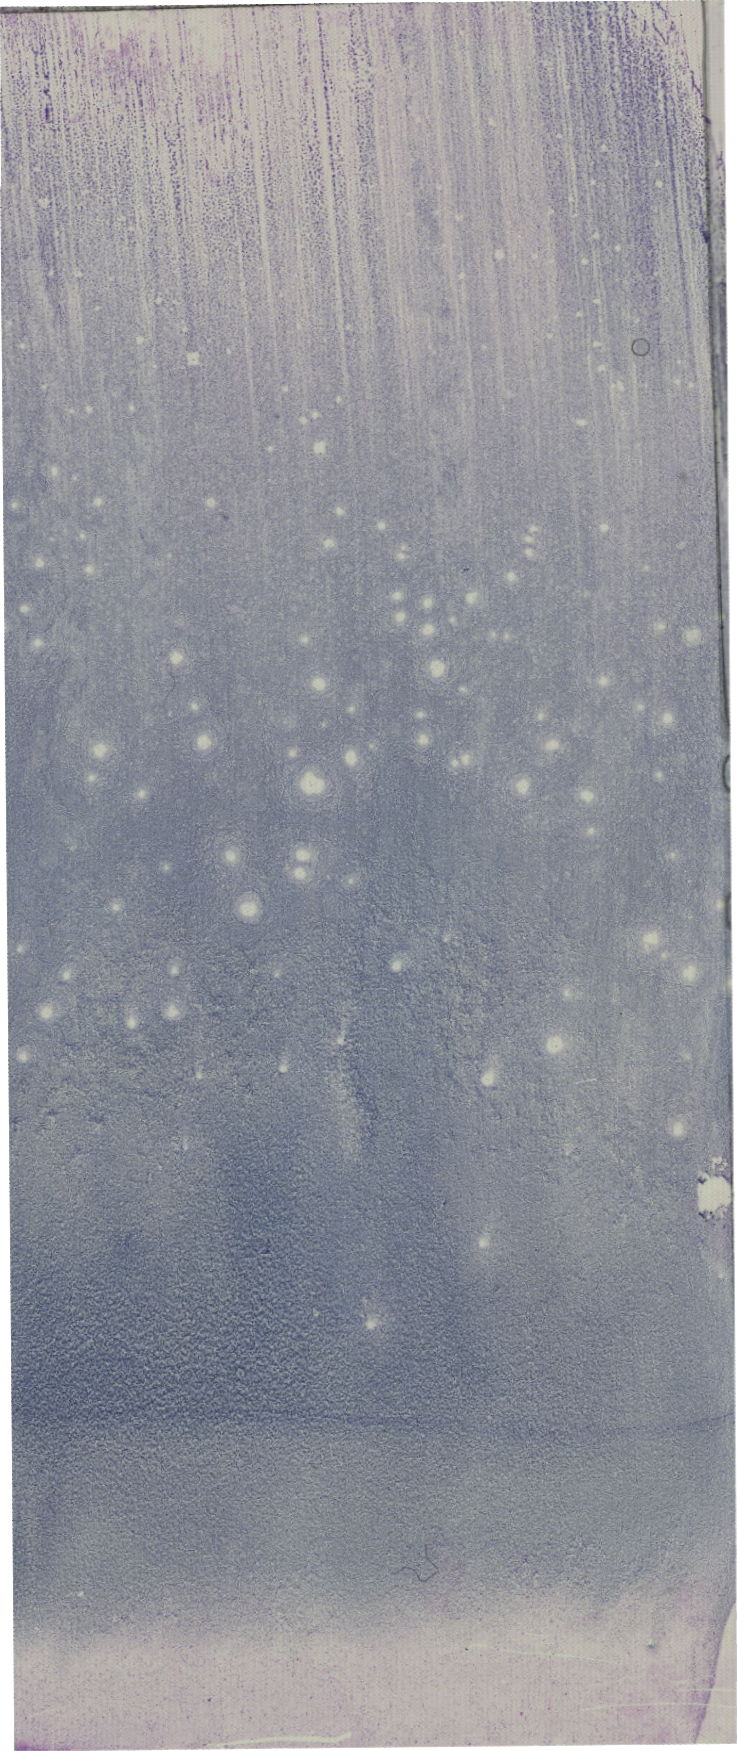
May-Grünwald-Giemsa (MGG)-stained marrow aspirate smear (whole slide), a low-resolution overview of the entire scanned area, about 20.9 x 49.6 mm. Female patient.
Diagnosis: B Acute Lymphoblastic Leukemia.